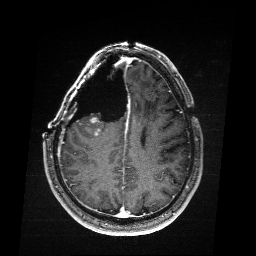
Brain MRI from a brain-tumour surgery series, one axial slice; T1-weighted post-contrast; 256 × 256 image matrix, field of view 256 × 256 mm. Case-level facts recorded for this patient, not image findings: histopathology: Astrocytoma; WHO grade: 4; IDH mutation: yes.
Outlined on this slice (manually delineated by an expert):
- residual tumour: bounding box (x1, y1, x2, y2) in pixels: (106, 118, 117, 136)